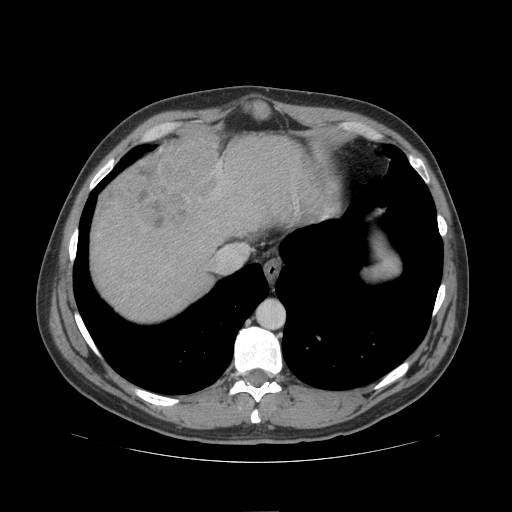
Contrast-enhanced abdominal CT (liver protocol), one axial slice. Slice 88 of 109 in the series (ordered by position). Reconstruction kernel STANDARD. Soft-tissue window (W 400 / L 40 HU). 2.5 mm slice thickness. 512 × 512 image matrix, field of view 420 × 420 mm. Case-level facts recorded for this patient, not image findings: diagnosis: hepatocellular carcinoma (patient treated with transarterial chemoembolisation; whether this scan precedes or follows treatment is not stated here); TNM stage (as recorded): Stage-IIIB; Child-Pugh class: A; tumour nodularity: multinodular.
Annotated regions visible in this slice (semi-automatically segmented with operator editing):
- liver parenchyma outside the tumour (the mass and vessels are separate outlines, so this box may not span the whole liver): bounding box (x1, y1, x2, y2) in pixels: (90, 134, 304, 320)
- mass: (111, 125, 224, 227)